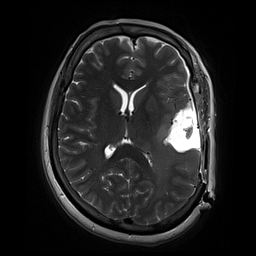
Brain MRI from a brain-tumour surgery series, one axial slice; position 35 of 70 along the scan axis; 256 × 256 image matrix, field of view 220 × 220 mm. Case-level facts recorded for this patient, not image findings: histopathology: Glioblastoma; WHO grade: 4; IDH mutation: no.
Structures marked on this image (manually delineated by an expert):
- residual tumour: bounding box <154,115,172,142> (left, top, right, bottom; pixels)